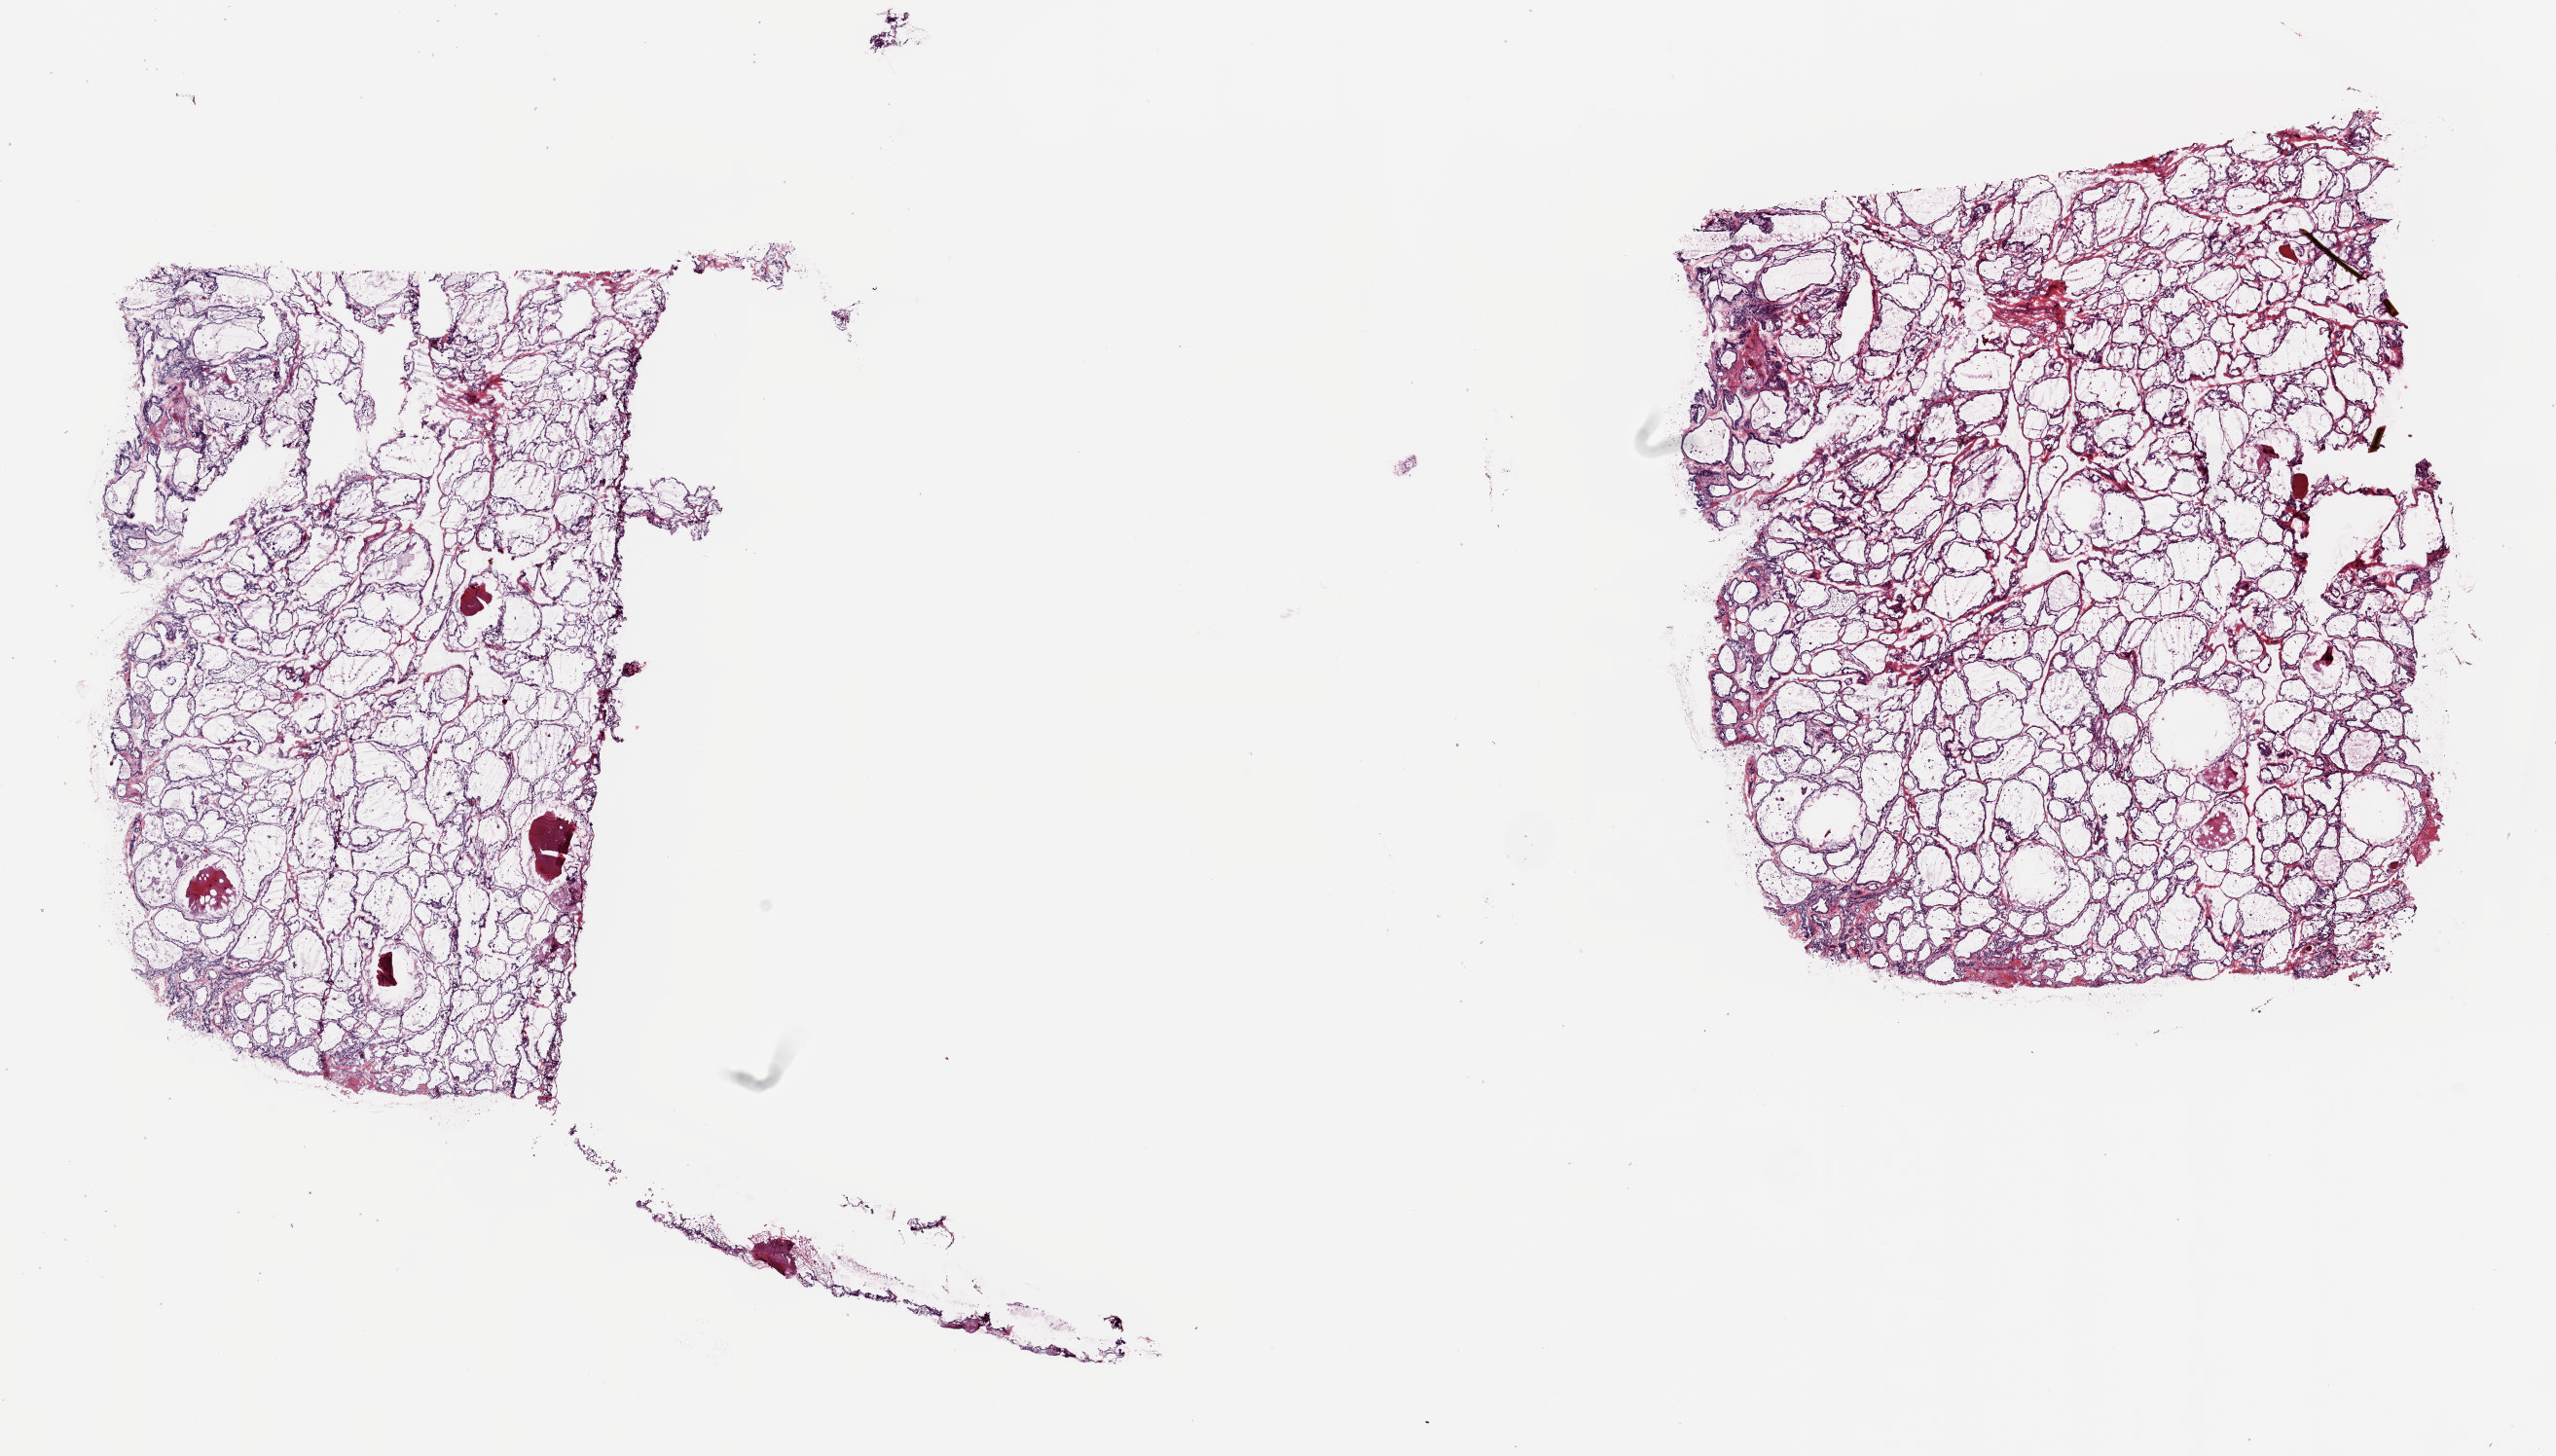
Digitized H&E-stained tissue section (whole slide) — whole scanned area (about 20.8 x 11.9 mm) shown as a low-resolution overview; frozen section from the top of the tissue portion; thyroid, solid tissue normal (non-tumour tissue) sample. Patient: male, age at initial diagnosis 36 years. Composition of this section per pathologist review: tumour cells 0%, tumour nuclei 0%, normal cells 100%, stromal cells 0%, necrosis 0%. Inflammatory infiltration, as recorded: lymphocyte infiltration 1%, monocyte infiltration 2%, neutrophil infiltration 0%.
- this section: solid tissue normal sample (biorepository sample class)
- patient diagnosis: Papillary carcinoma, follicular variant (thyroid gland)